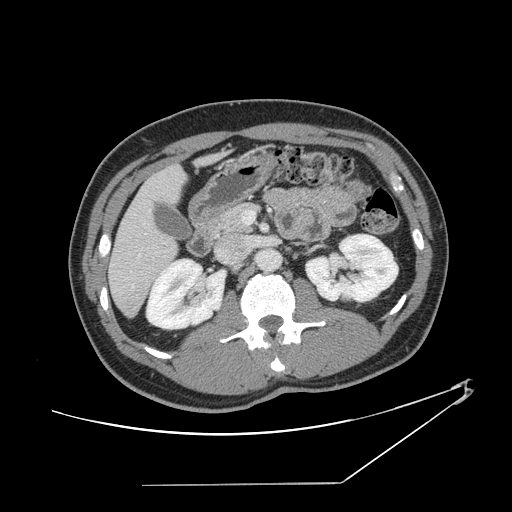
Contrast-enhanced abdominal CT, one axial slice; slice 65 of 152 in the series (ordered by position); 120 kVp; soft-tissue window (W 400 / L 40 HU); 2.5 mm slice thickness; 512 × 512 image matrix, field of view 432 × 432 mm. Male patient, age 45 years. From the clinical record (not read from this slice): diagnosis: colorectal cancer liver metastases, imaged before liver resection; multiple liver metastases: no; largest metastasis: 1 cm.
Structures marked on this image (outlined manually by an expert reader):
- hepatic veins: box from (x=138, y=210) to (x=157, y=258) px
- liver: (x=110, y=157)–(x=216, y=315)
- planned liver remnant (the part of the liver to remain after resection): (x=110, y=167)–(x=184, y=316)
- portal vein (with intrahepatic branches): (x=242, y=211)–(x=255, y=224)